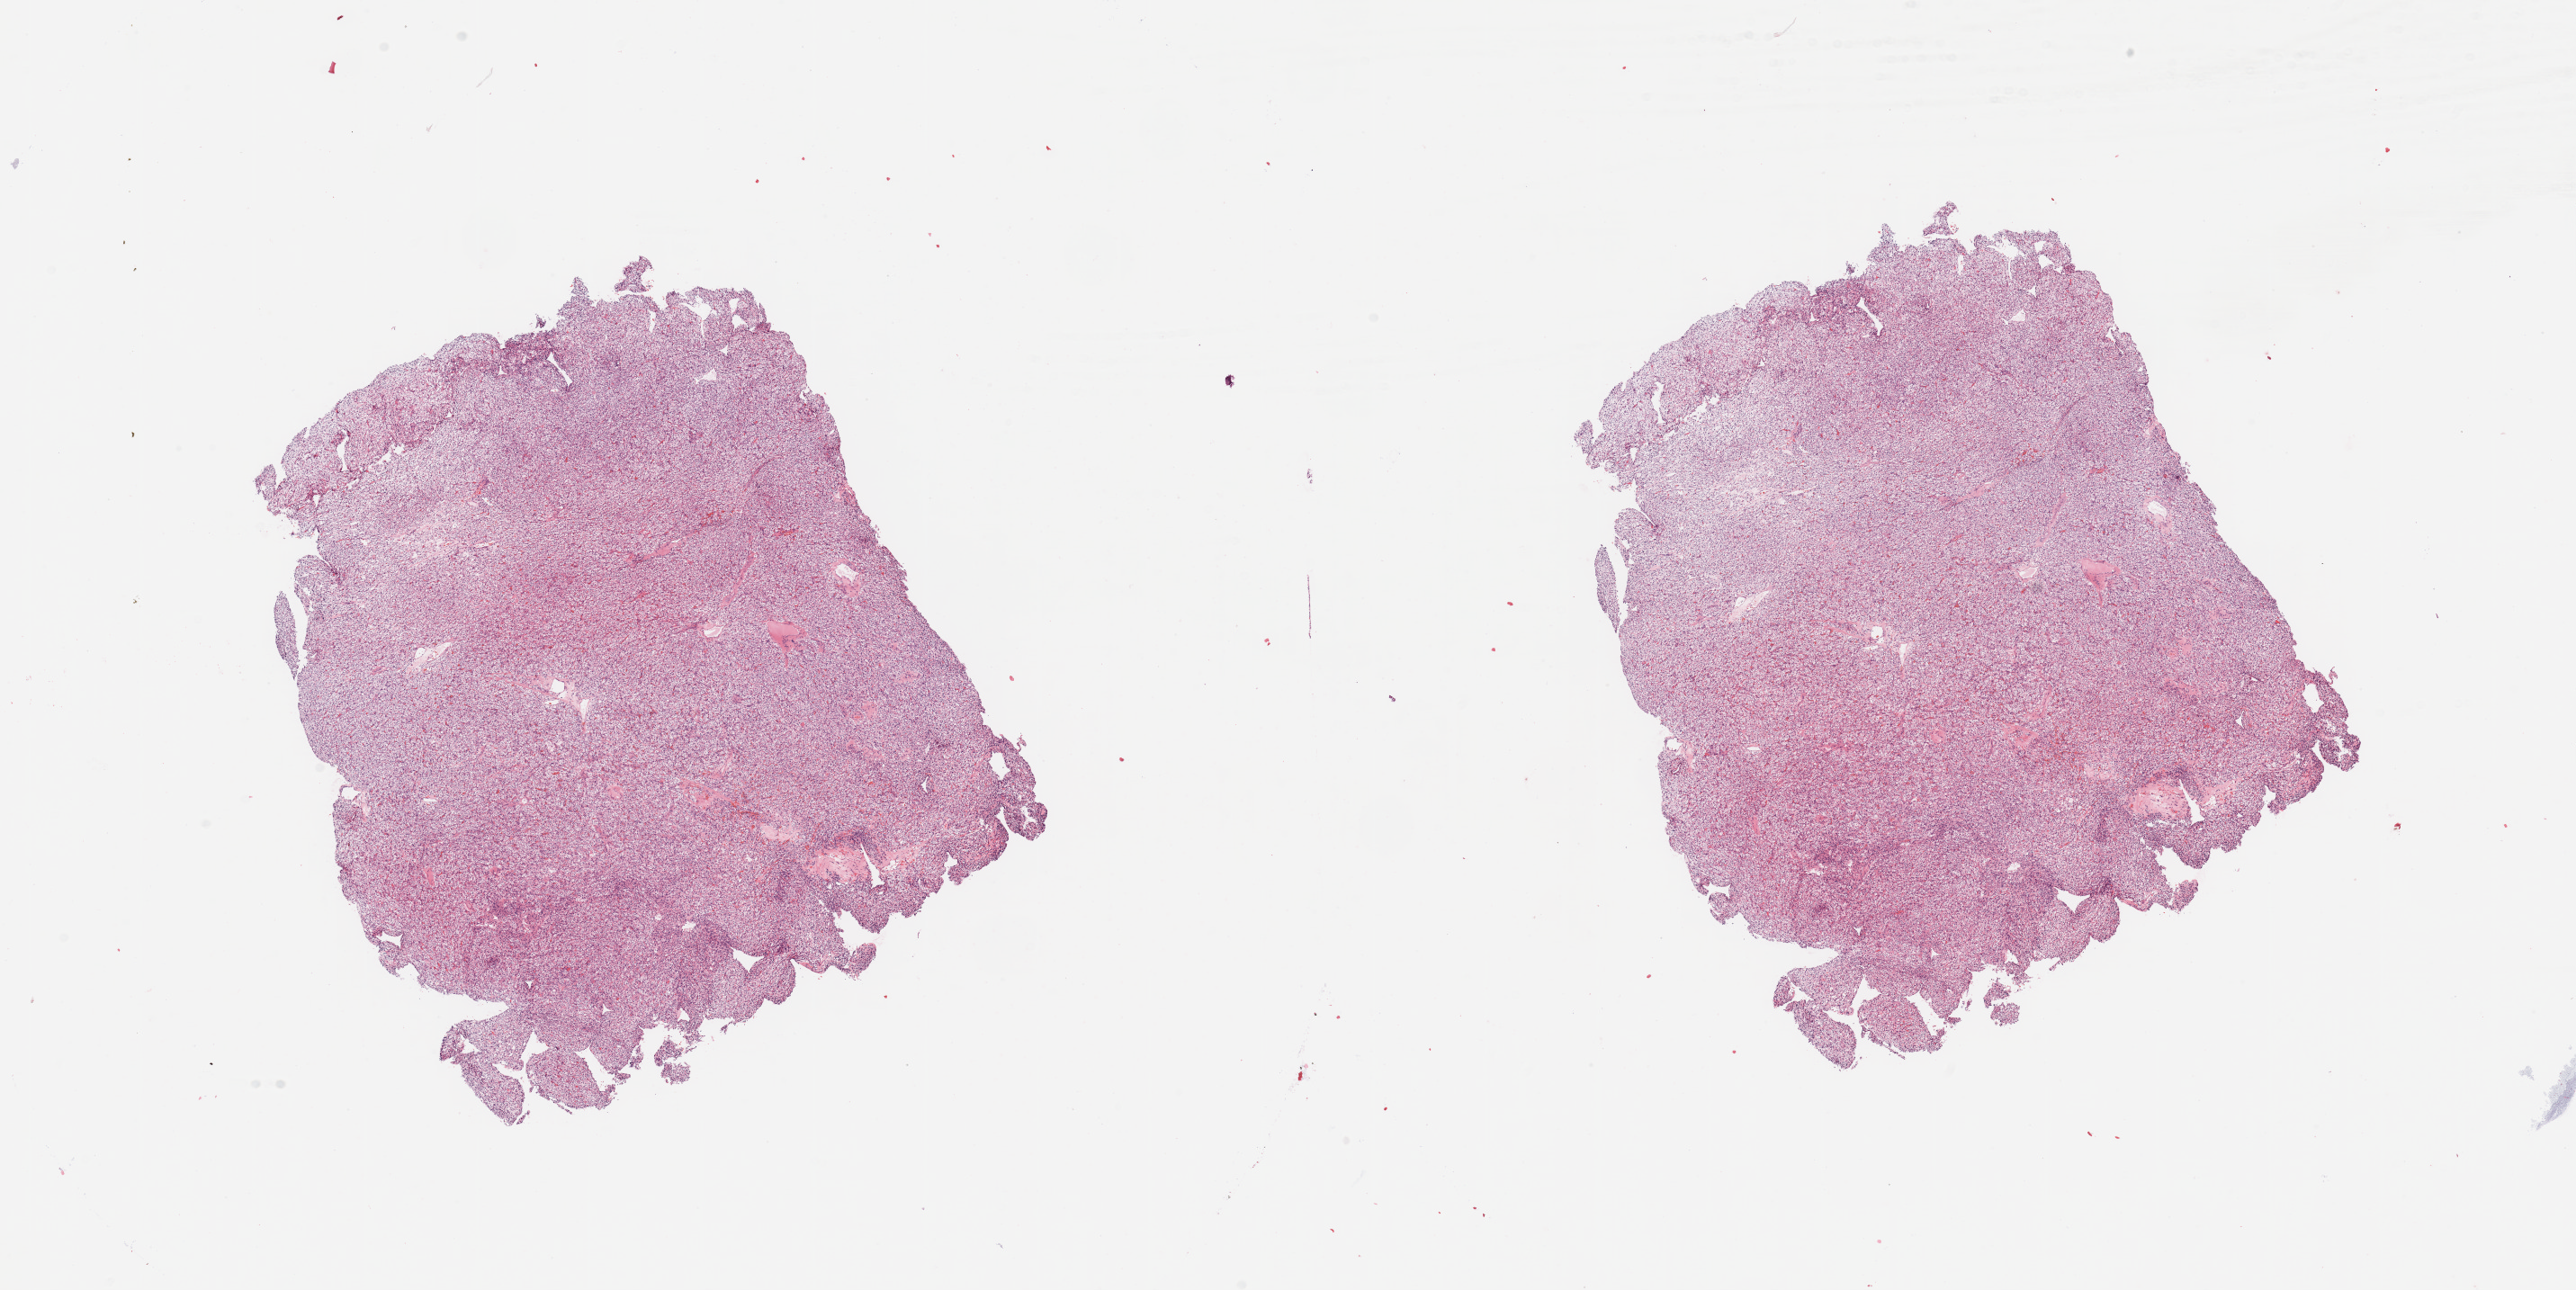
H&E whole-slide image — low-resolution overview of the scanned area, about 22.6 x 11.3 mm (from a 20x scan); tumour tissue sample, sampled site: kidney. Patient: female, age 70 years. Composition of this section per pathologist review: tumour nuclei 90%, necrosis 3%.
Diagnosis: Renal cell carcinoma, NOS.